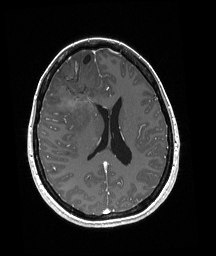
Brain MRI from a brain-tumour surgery series, one axial slice. Slice 83 of 192 in the series (ordered by position). T1-weighted post-contrast. 1 mm slice thickness. 216 × 256 image matrix, field of view 211 × 250 mm. Case-level facts recorded for this patient, not image findings: histopathology: Oligodendroglioma; WHO grade: 3; IDH mutation: yes; tumour location: Right Frontal.
Annotated regions visible in this slice (outlined manually by an expert reader):
- tumour: box from (x=55, y=80) to (x=98, y=110) px